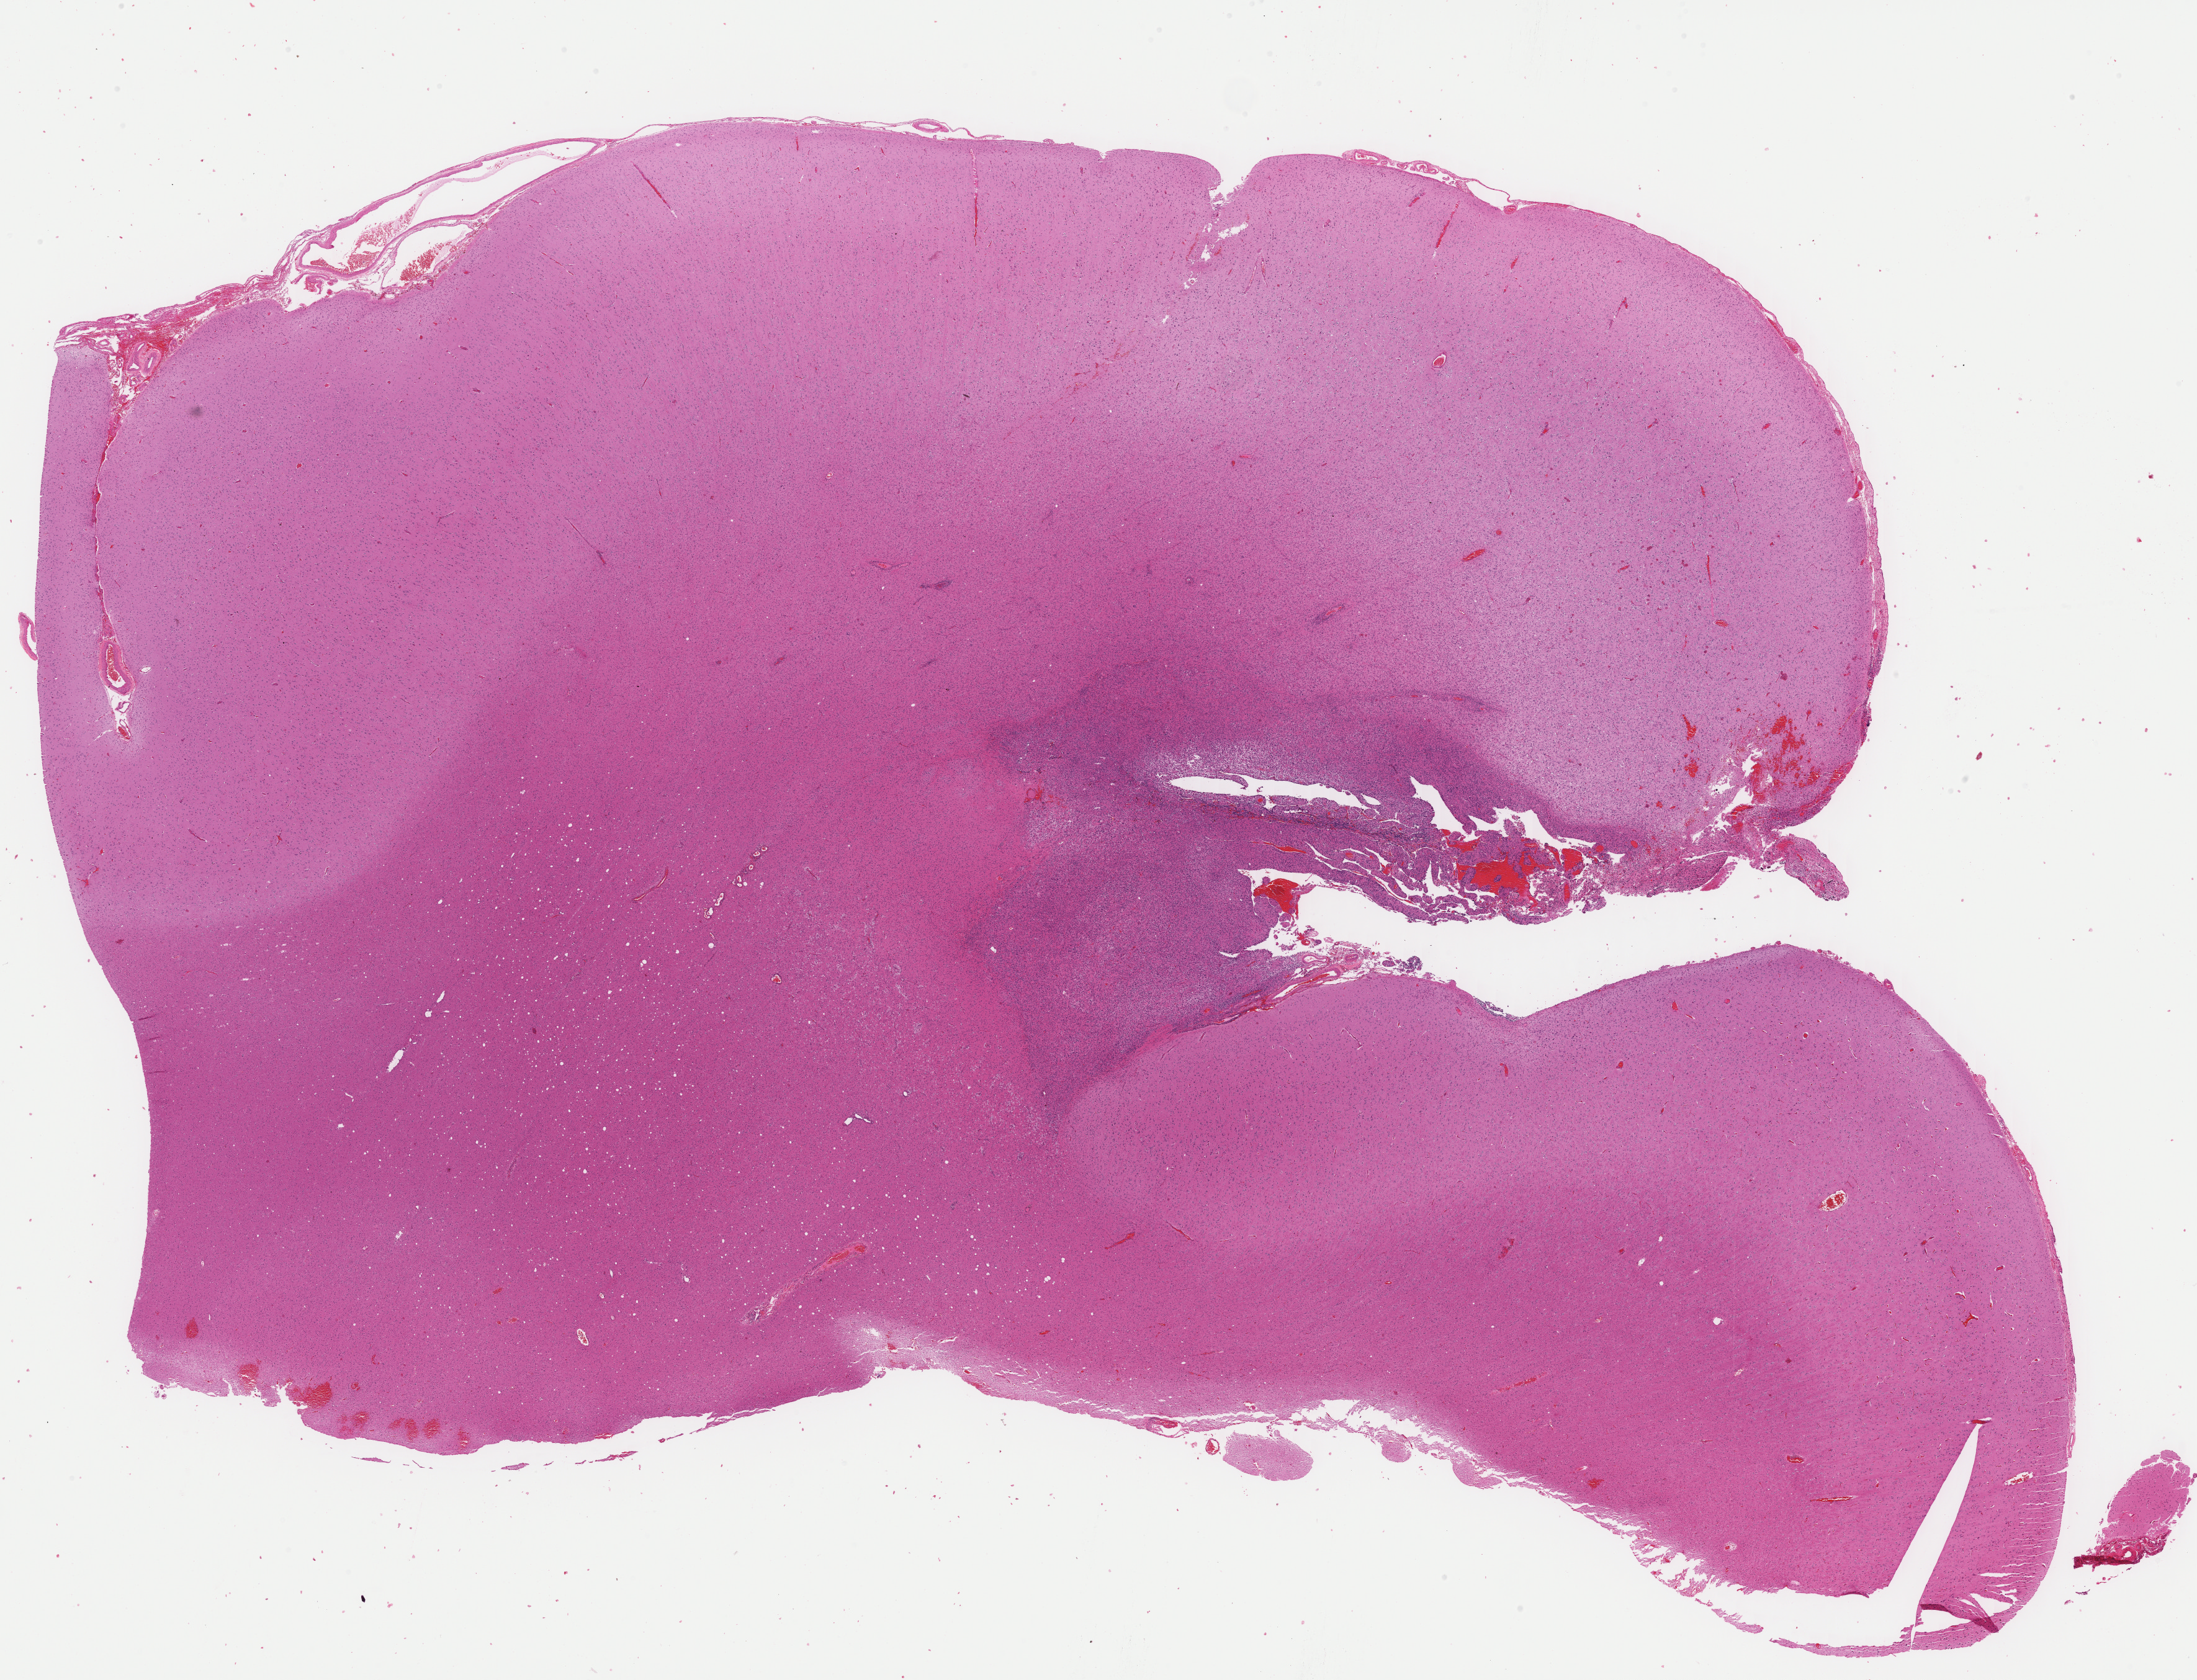
Whole-slide histology image, H&E-stained — whole scanned area (about 27.9 x 21.3 mm) shown as a low-resolution overview, formalin-fixed paraffin-embedded (FFPE) diagnostic section, brain, primary tumour sample. Female, age 38 years at initial diagnosis. Histologic grade: G3 (poorly differentiated).
* laterality: left
* diagnosis: Mixed glioma (cerebrum)